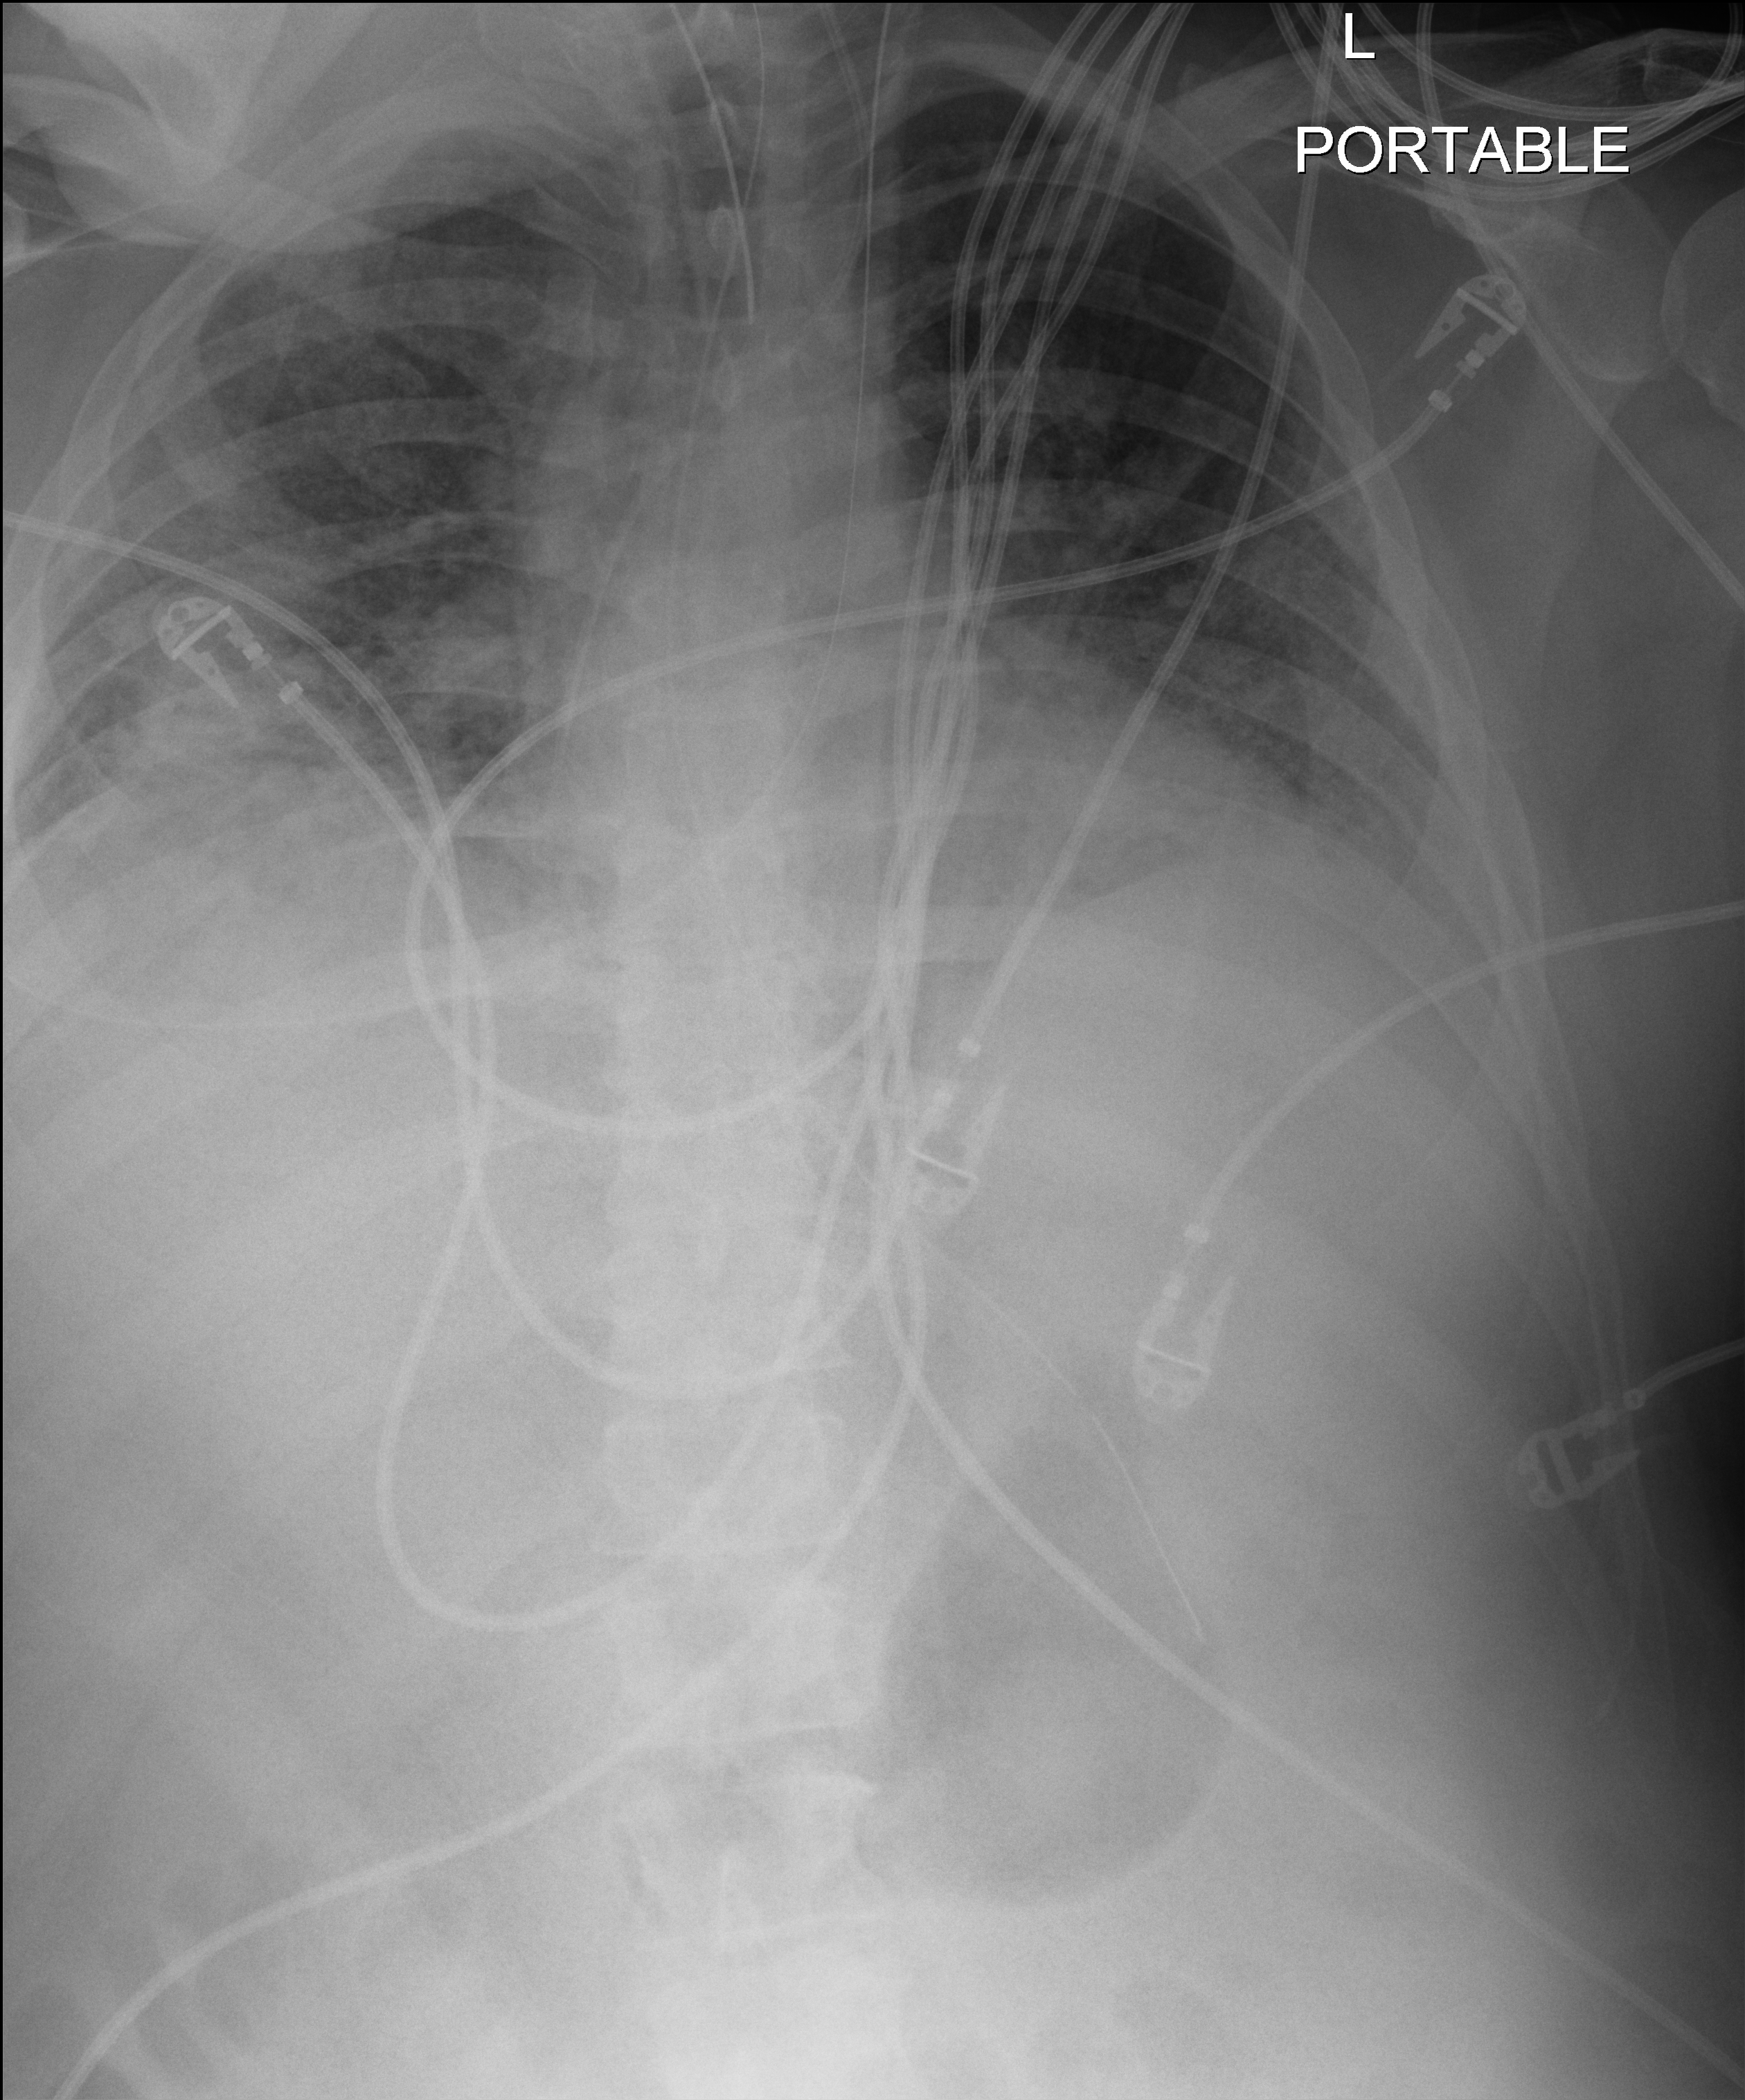
Portable chest radiograph. Male patient hospitalised with COVID-19, age 18–59 years.
From the hospital-stay record, not from the radiograph (when in the stay this image was taken is not recorded): hypertension (admission record): yes; chronic kidney disease (admission record): no.